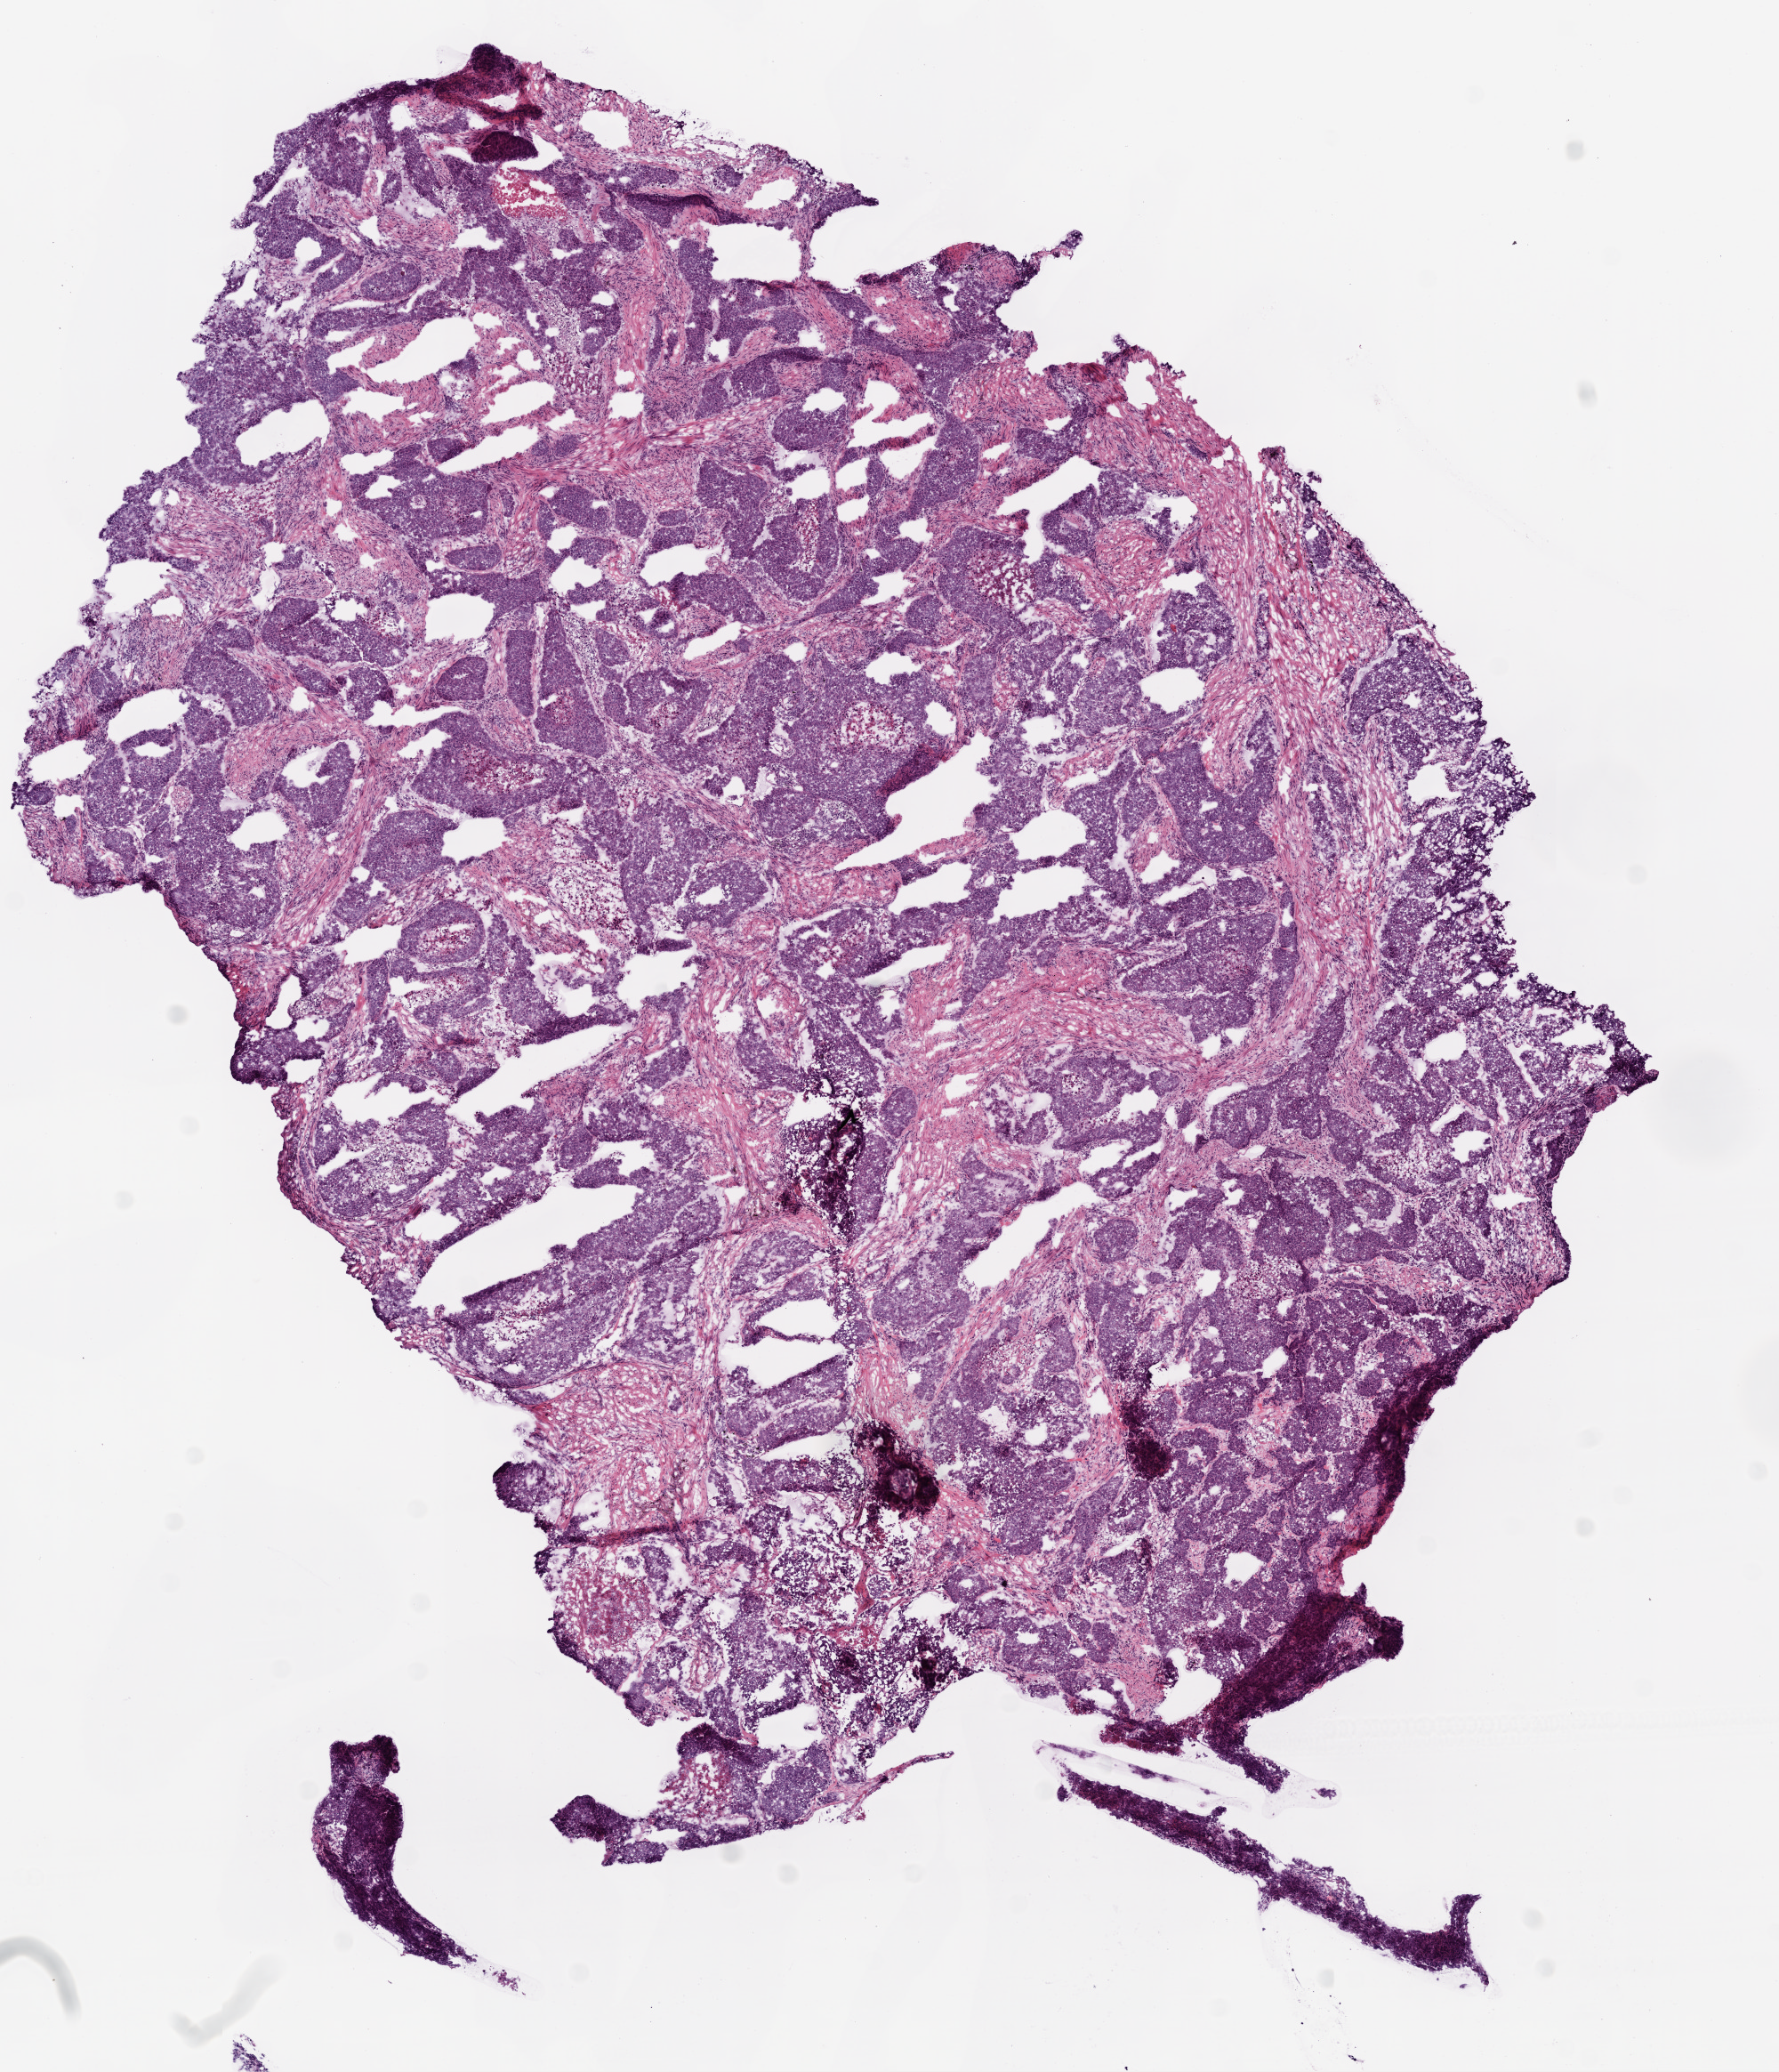
Whole-slide histology image, Hematoxylin and eosin (H&E) stained — low-resolution overview of the scanned area, about 8.0 x 9.3 mm. Frozen section from the top of the tissue portion. Lung, primary tumour sample. Male patient; age at initial diagnosis 68 years. Slide review estimates, as recorded: tumour cells 77%, tumour nuclei 85%, normal cells 0%, stromal cells 15%, necrosis 8%.
* laterality: left
* AJCC pathologic stage: IIIB (6th edition)
* diagnosis: Squamous cell carcinoma, NOS (upper lobe, lung)